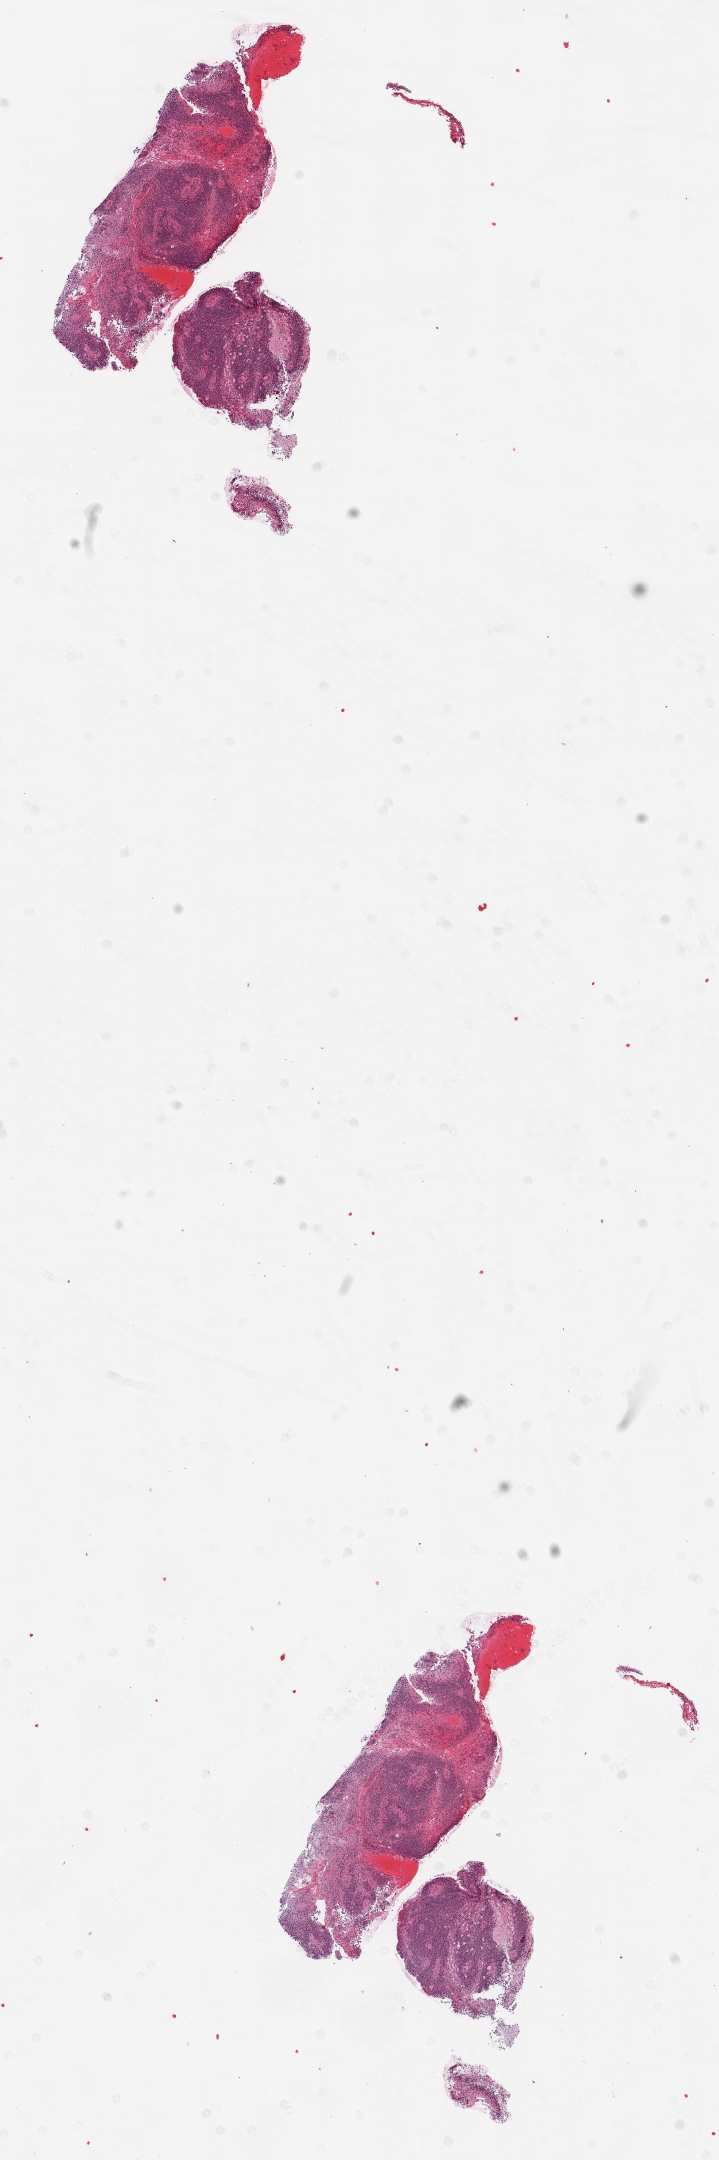
H&E-stained whole-slide image, low-resolution overview of the scanned area, about 5.8 x 17.4 mm (from a 20x scan), formalin-fixed paraffin-embedded (FFPE) diagnostic section, primary tumour sample from the brain. Male patient; age at initial diagnosis 69 years.
Pathologic diagnosis: Glioblastoma.